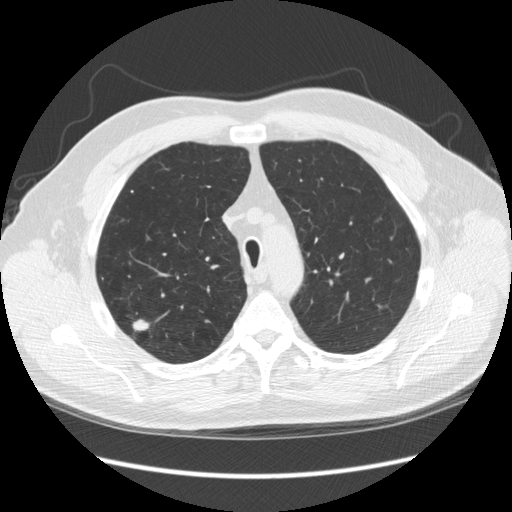
Low-dose screening chest CT, axial slice. Third annual screen. Lung window (W 1500 / L -600 HU). 2.5 mm slice thickness. Slice 58 of 248 in the series. Male, age 64 years at enrolment. Former smoker at enrolment.
• Lesion marked by an expert reader, bounding box (x1, y1, x2, y2) in pixels: (118, 313, 168, 354).
• The screening reader recorded 4 non-calcified nodules or masses ≥4 mm on this exam; which of them this box marks is not recorded.
• Official screen result: positive, other.
• Participant outcome: lung cancer diagnosed 15 days after this screen — adenocarcinoma, NOS, right upper lobe, moderately differentiated (G2), stage IA (AJCC 6th edition), 14 mm at pathology.